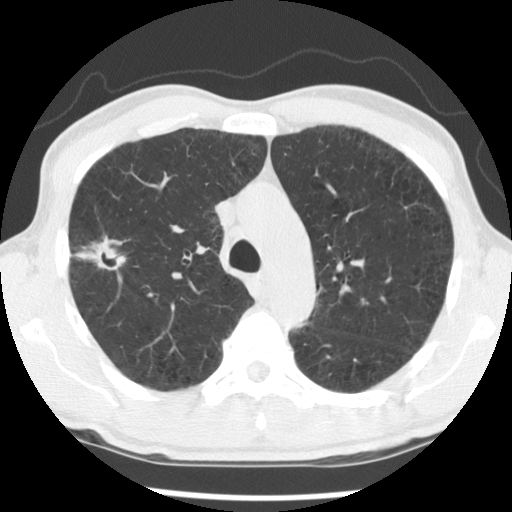
Axial slice from a low-dose chest CT screening exam; second screening round (one year after baseline); lung window (W 1500 / L -600 HU); standard (soft-tissue) reconstruction kernel (STANDARD); slice 92 of 138 in the series. Male participant, aged 56 years at enrolment. Current smoker at enrolment.
Lesion marked by an expert reader, bounding box [x1, y1, x2, y2] px = [55, 231, 141, 296]. The exam's reader record, not a measurement of the box and not confirmed to be the same lesion: non-calcified nodule or mass ≥4 mm, right upper lobe, 30 × 18 mm, spiculated (stellate) margins, mixed attenuation, pre-existing on the prior screen: yes; interval growth: yes. Official screen result: positive, other. Participant outcome: lung cancer diagnosed 326 days after this screen — squamous cell carcinoma, NOS, right upper lobe, right middle lobe, moderately differentiated (G2), stage IB (AJCC 6th edition), 70 mm at pathology.